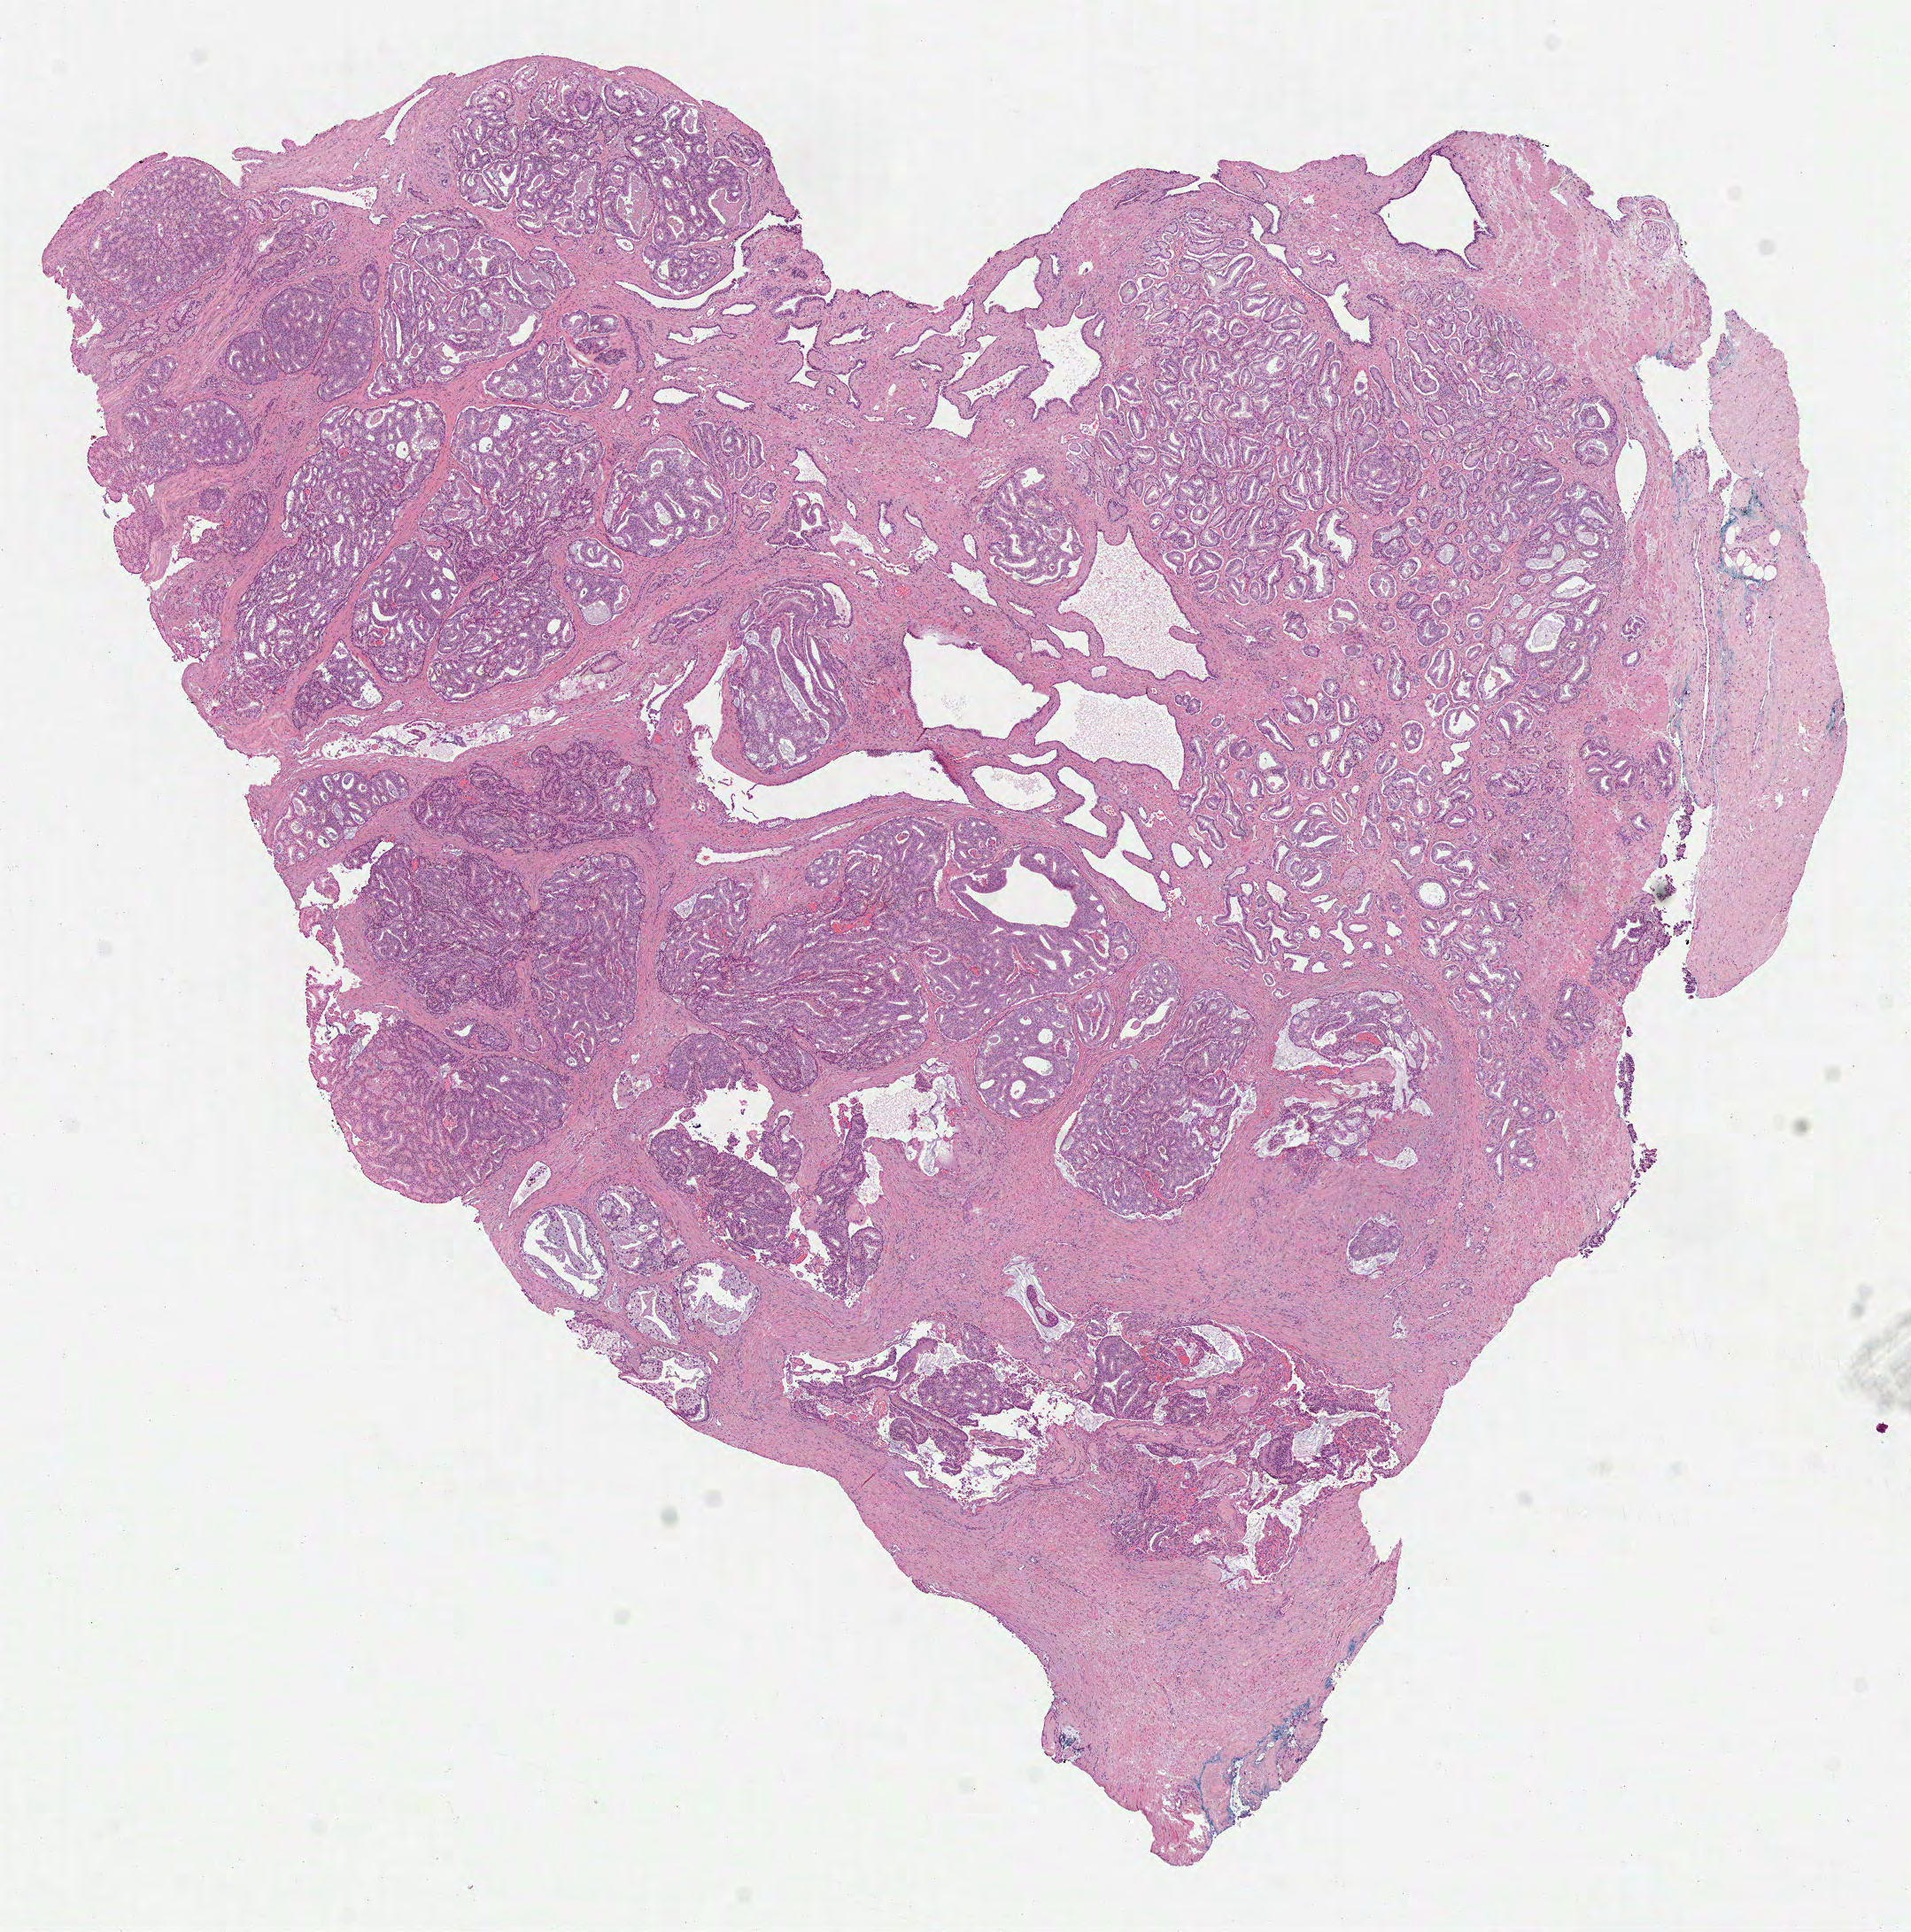
Digitized H&E tissue section (whole slide), low-resolution overview of the scanned area, about 8.7 x 8.8 mm, formalin-fixed paraffin-embedded (FFPE) diagnostic section, sample: primary tumour, prostate. Patient: male, age at initial diagnosis 56 years. Gleason score: 7 (3+4).
* lymph nodes positive (case pathology): 0 of 4 examined
* histologic diagnosis: Acinar cell carcinoma
* laterality: right